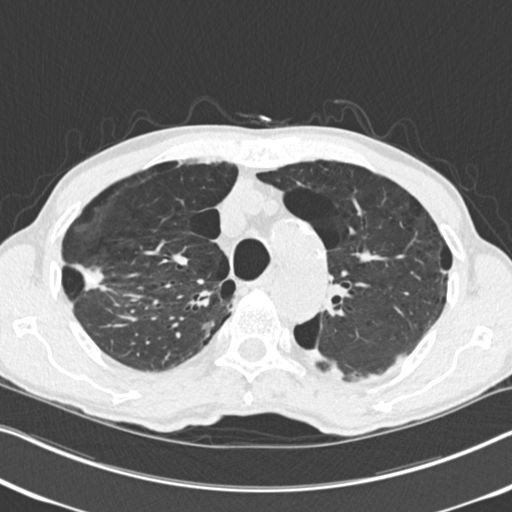
Chest CT (low-dose screening protocol), one axial image; second screening round (one year after baseline); lung window (W 1500 / L -600 HU); standard (soft-tissue) reconstruction kernel (B30f); 512 × 512 image matrix, field of view 334 × 334 mm. Male, age 71 years at enrolment. Current smoker at enrolment.
Expert reader's lesion annotation, bounding box (x1, y1, x2, y2) in pixels: (59, 242, 130, 317). The screening reader recorded 4 non-calcified nodules or masses ≥4 mm on this exam (right upper lobe, right upper lobe, right upper lobe, left upper lobe); which of them this box marks is not recorded. Official screen result: positive, change unspecified: nodule(s) >= 4 mm or enlarging nodule(s), mass(es), or other non-specific abnormalities suspicious for lung cancer.